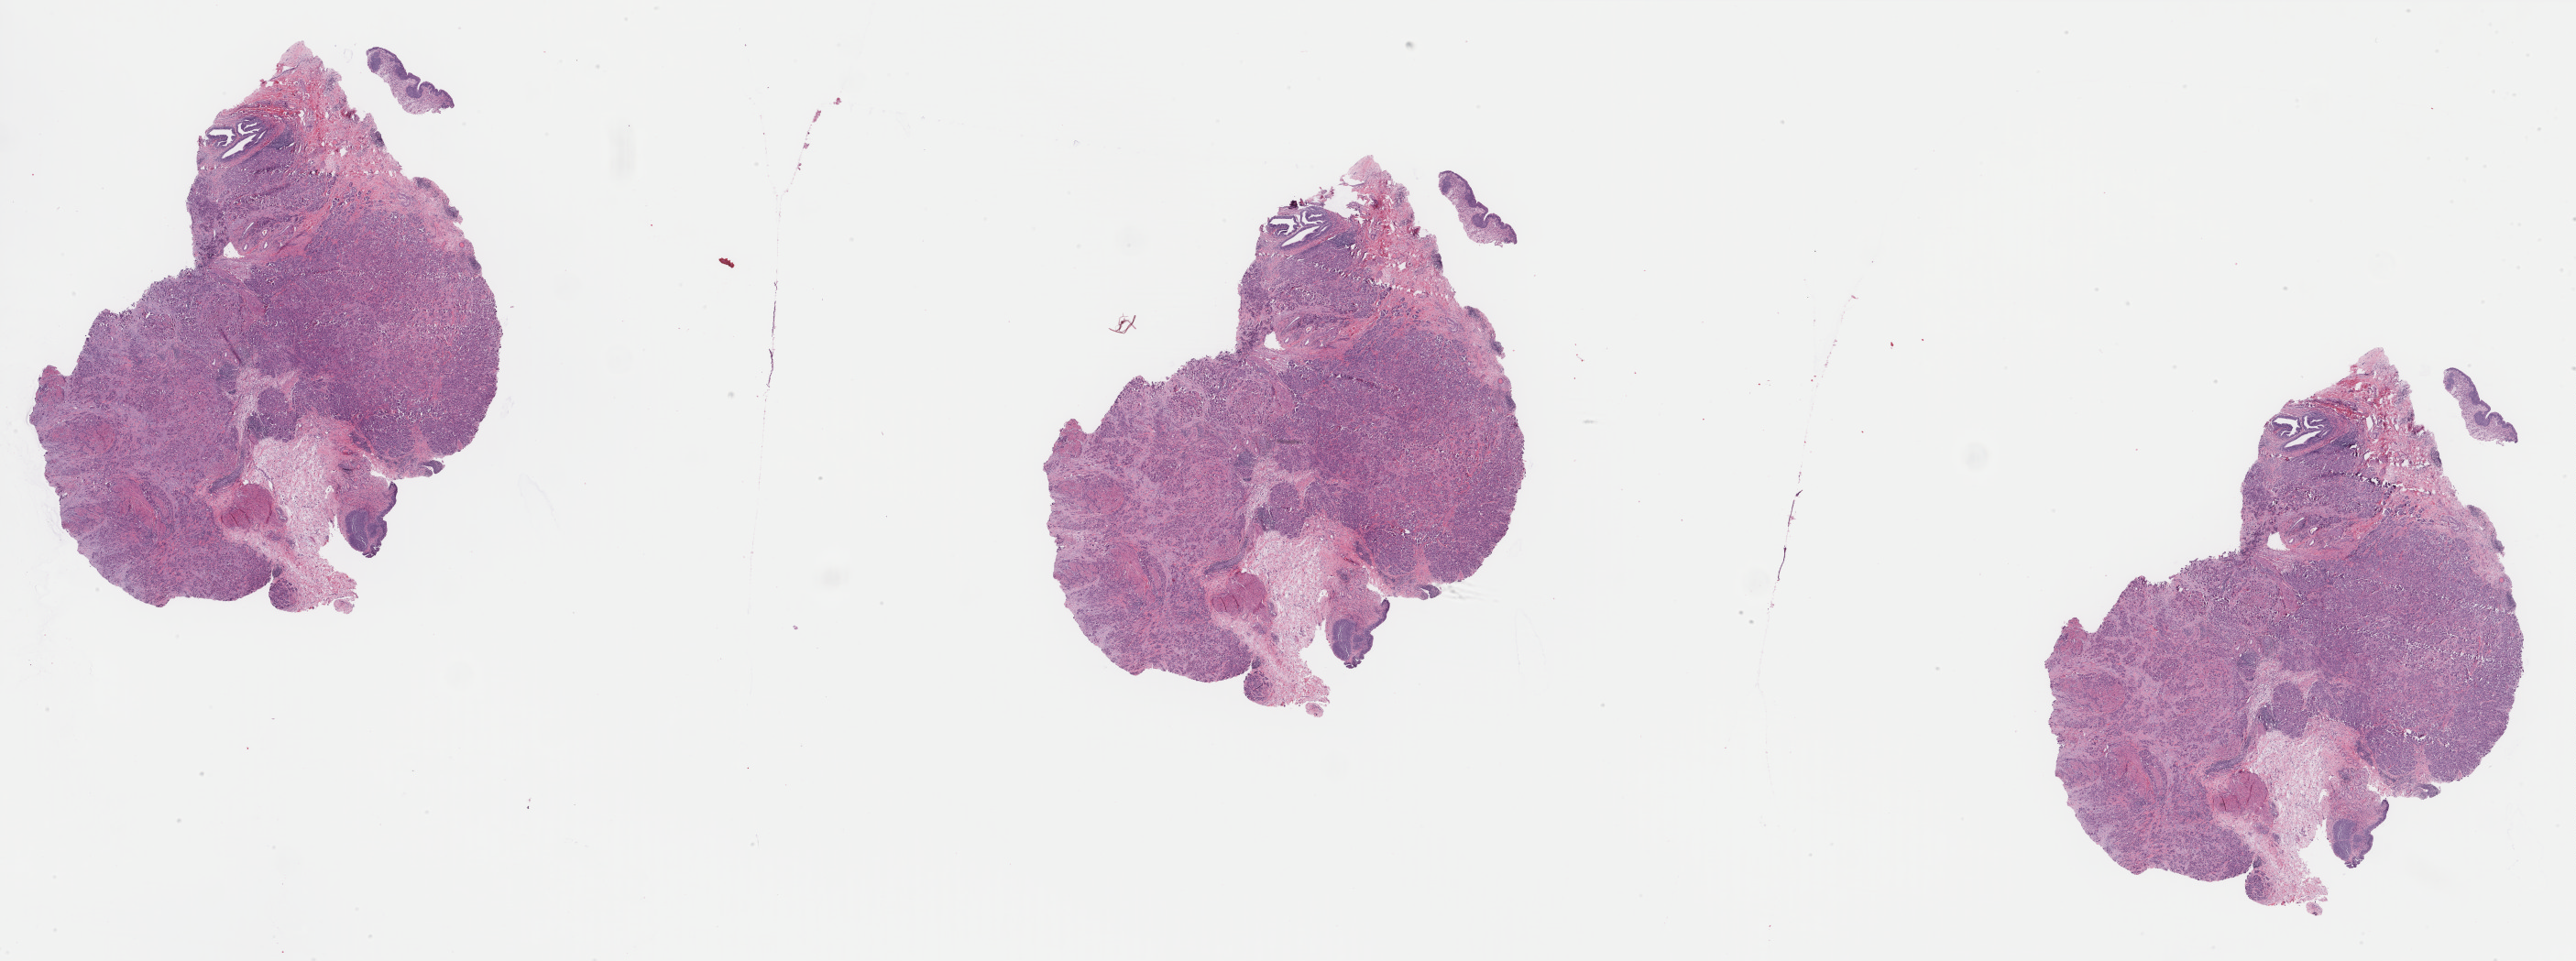
Digitized H&E-stained tissue section (whole slide), shown as a low-resolution overview of the whole scanned area (about 44.6 x 16.7 mm); FFPE section; bladder, primary tumour sample. Patient: female, age at initial diagnosis 84 years. Histologic grade: high grade.
Pathologic diagnosis: Transitional cell carcinoma. AJCC pathologic stage: IV (7th edition). Lymph nodes positive (case pathology): 4 of 5 examined.